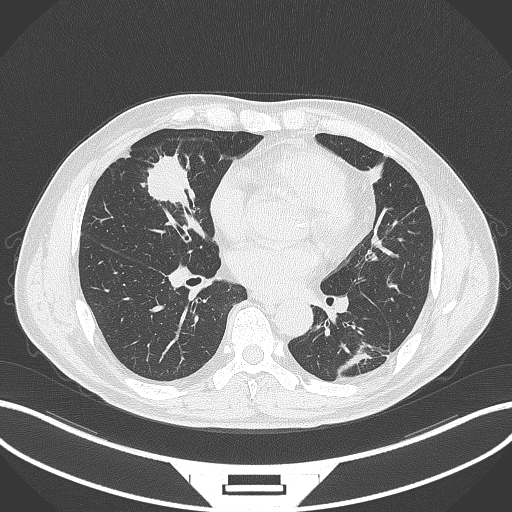
Chest CT, one axial slice. Position 131 of 399 along the scan axis. Reconstruction kernel B70f. Lung window (W 1500 / L -600 HU). 512 × 512 image matrix, field of view 400 × 400 mm. Patient: male, 59 years. From the clinical record (not read from this slice): clinical TNM (as recorded): T2a N1 M0.
Annotated regions visible in this slice (rectangle marked by the reading radiologist):
- lung tumour (recorded histology: adenocarcinoma): bounding box <143,150,198,210> (left, top, right, bottom; pixels)